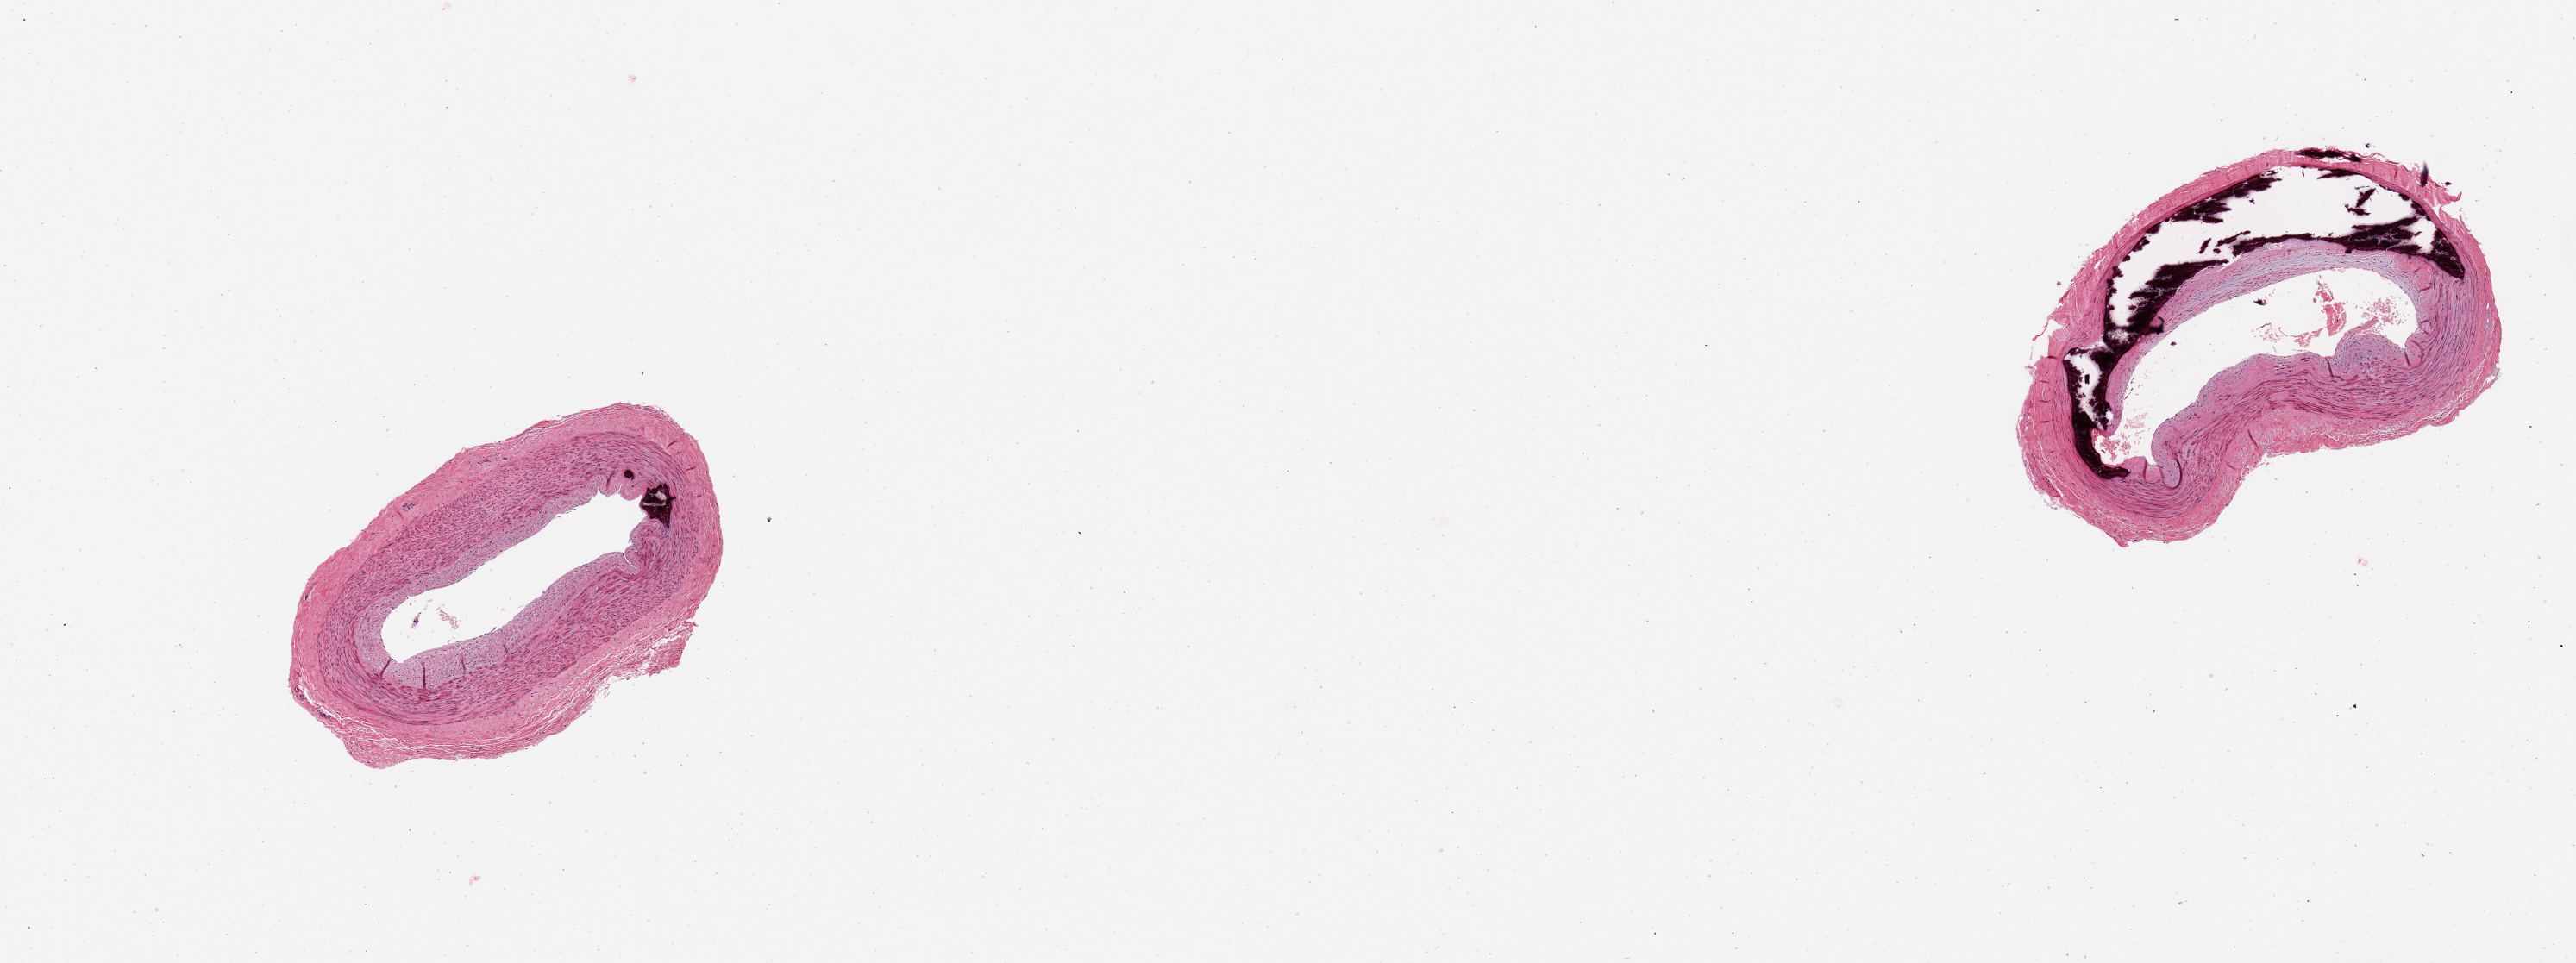
Whole-slide image, hematoxylin and eosin (H&E) stain — shown as a low-resolution overview of the whole scanned area (about 11.8 x 4.4 mm); PAXgene-fixed paraffin-embedded (PFPE) section; target tissue: tibial artery; donor tissue sample. Donor: male.
Reviewer comment on this tissue sample: 2 pieces, prominent Monckeberg medical sclerosis.